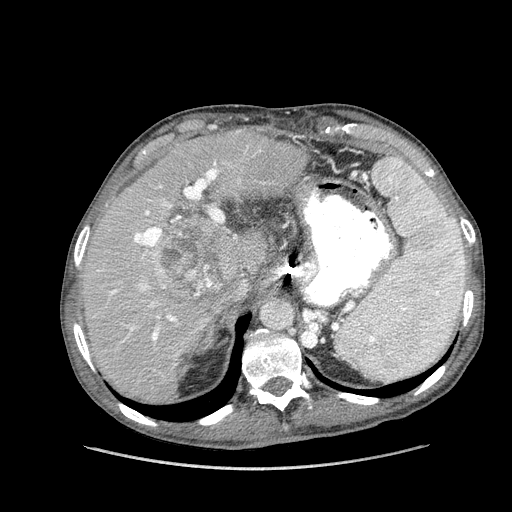
Contrast-enhanced abdominal CT (liver protocol), one axial slice; slice 101 of 162 in the series (ordered by position); reconstruction kernel STANDARD; 100 kVp; soft-tissue window (W 400 / L 40 HU); 2.5 mm slice thickness; 512 × 512 image matrix, field of view 400 × 400 mm. From the clinical record (not read from this slice): diagnosis: hepatocellular carcinoma (patient treated with transarterial chemoembolisation; whether this scan precedes or follows treatment is not stated here); TNM stage (as recorded): Stage-IIIA; Child-Pugh class: A; tumour nodularity: multinodular; tumour size: 9.9 cm.
Structures marked on this image (semi-automatically segmented with operator editing):
- liver parenchyma outside the tumour (the mass and vessels are separate outlines, so this box may not span the whole liver): bounding box [x1, y1, x2, y2] px = [82, 128, 306, 402]
- mass: [152, 213, 240, 305]
- liver vessels: [94, 146, 249, 343]